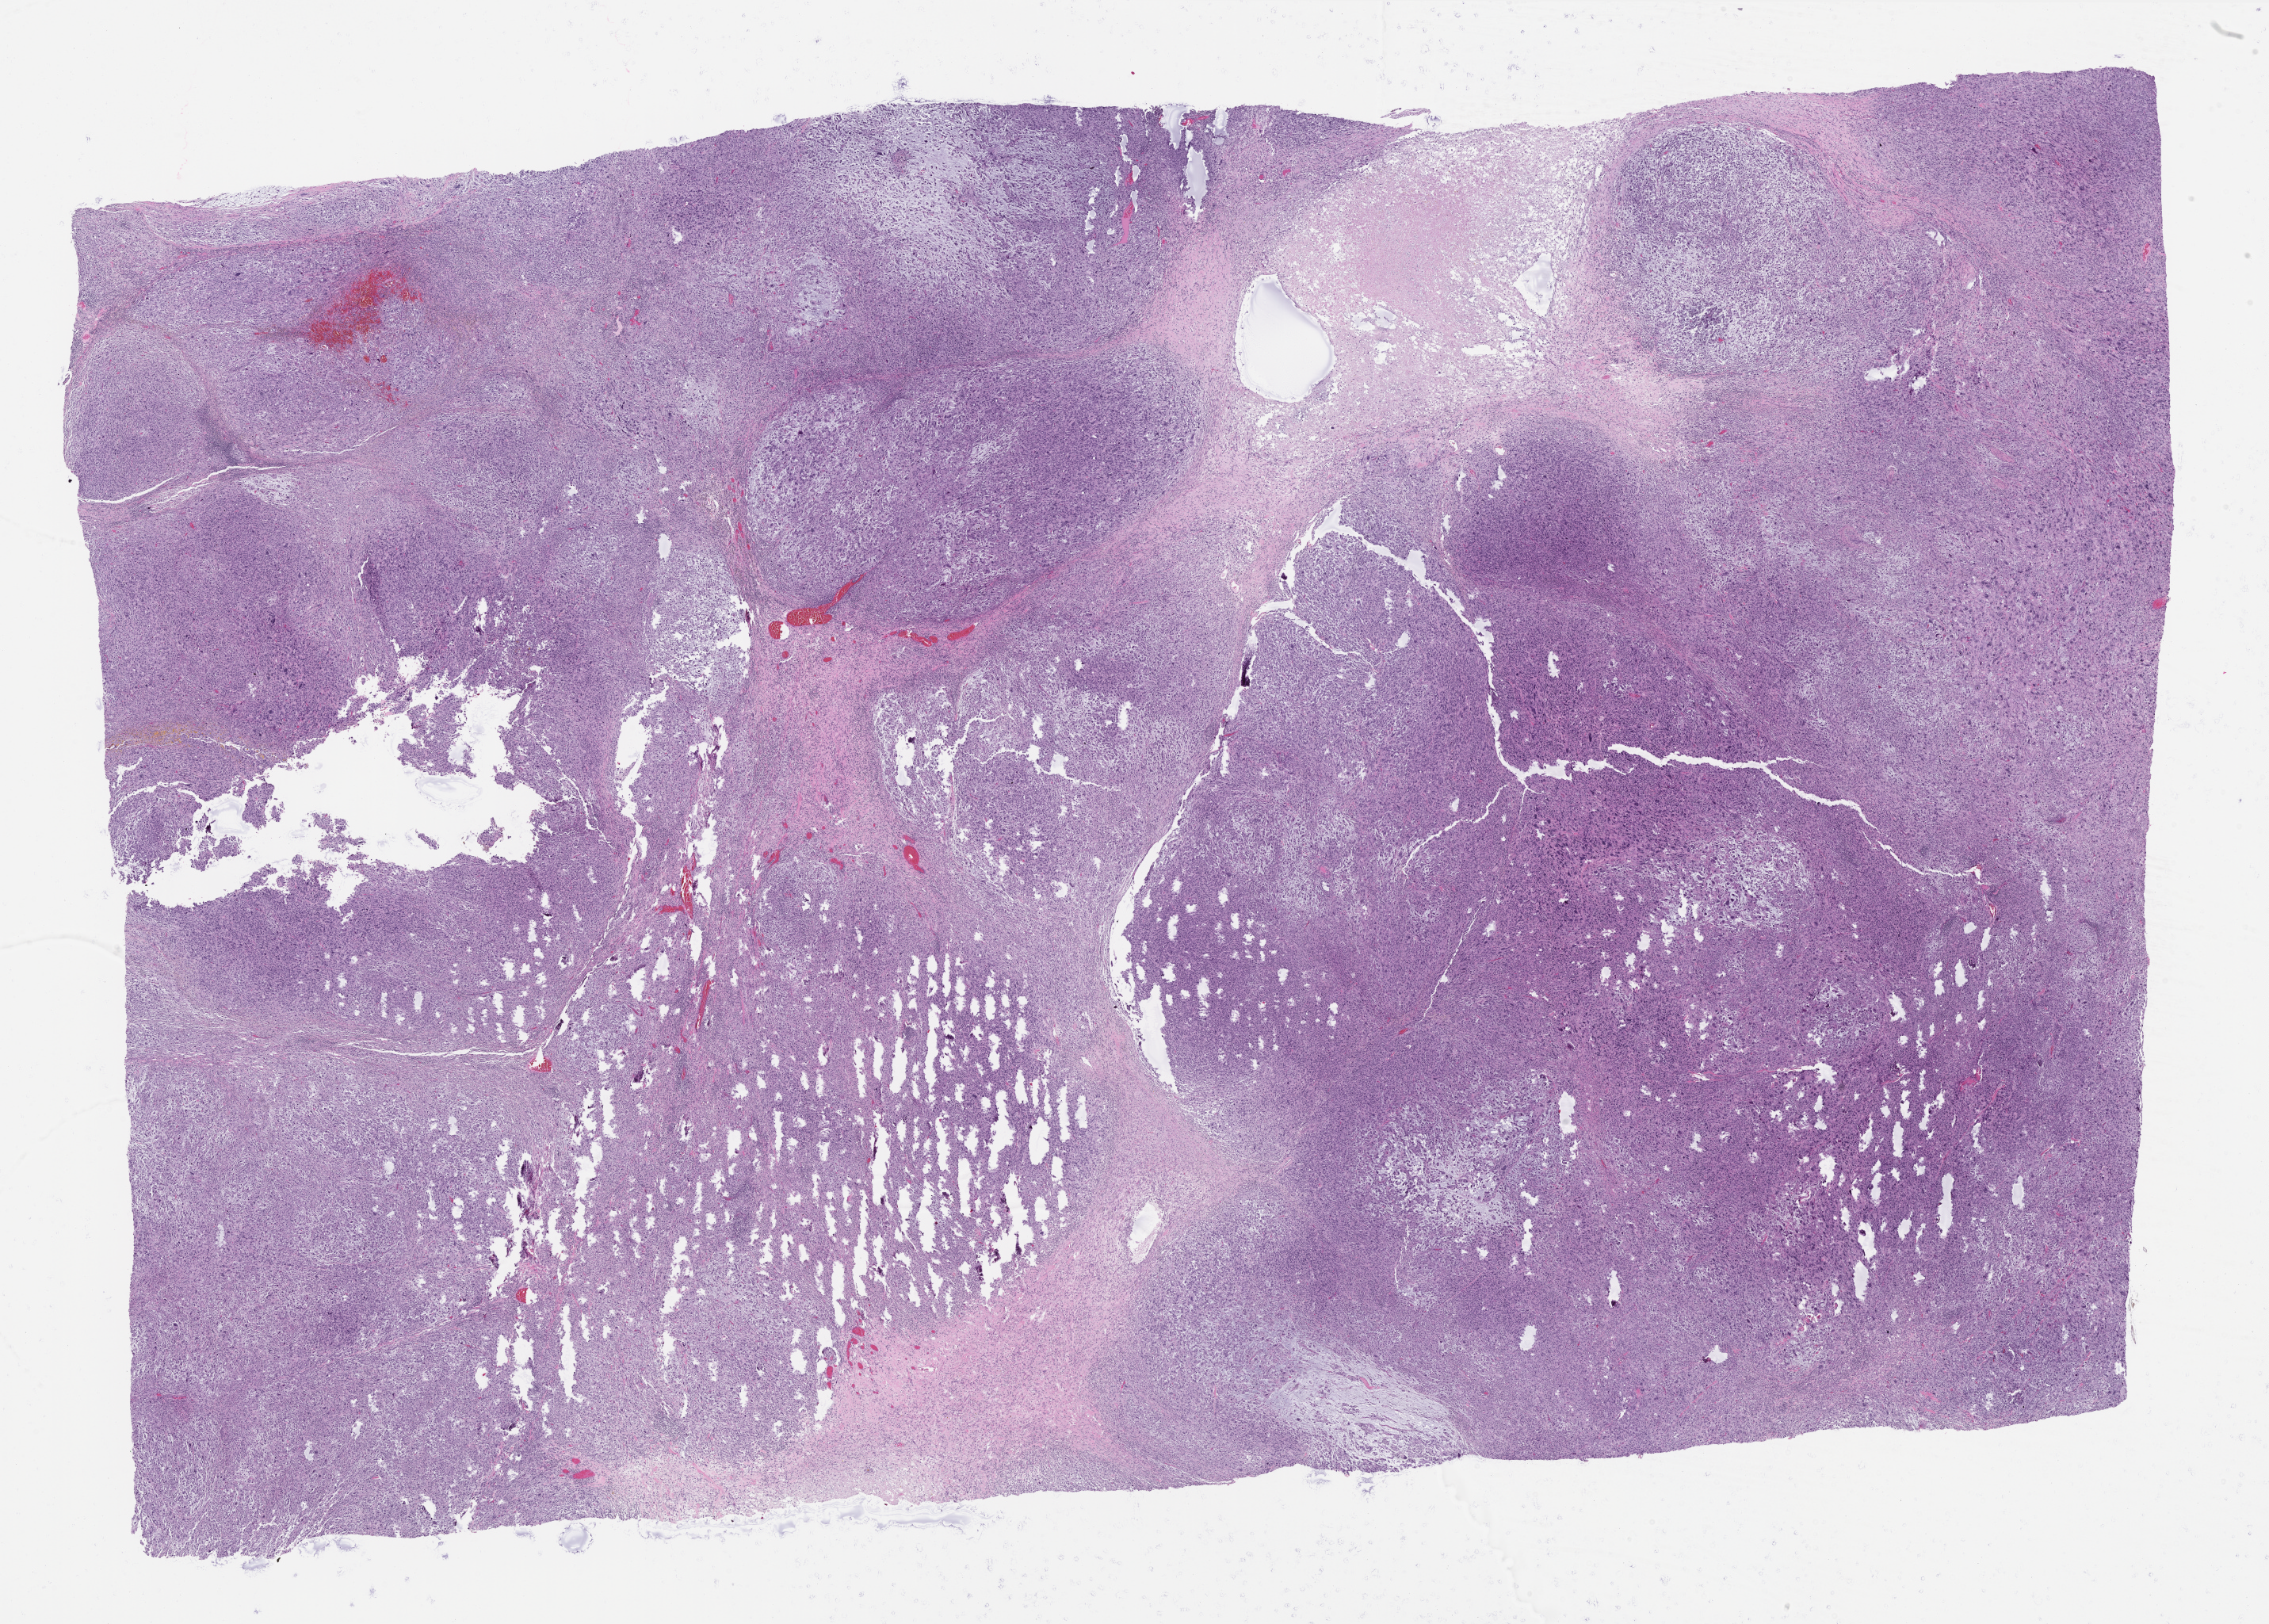
Whole-slide histology image, H&E — shown as a low-resolution overview of the whole scanned area (about 23.0 x 16.5 mm); formalin-fixed paraffin-embedded (FFPE) diagnostic section; sample: primary tumour, connective, subcutaneous and other soft tissues. Patient: male, age at initial diagnosis 86 years.
Pathologic diagnosis: Undifferentiated sarcoma (connective, subcutaneous and other soft tissues of trunk, NOS).